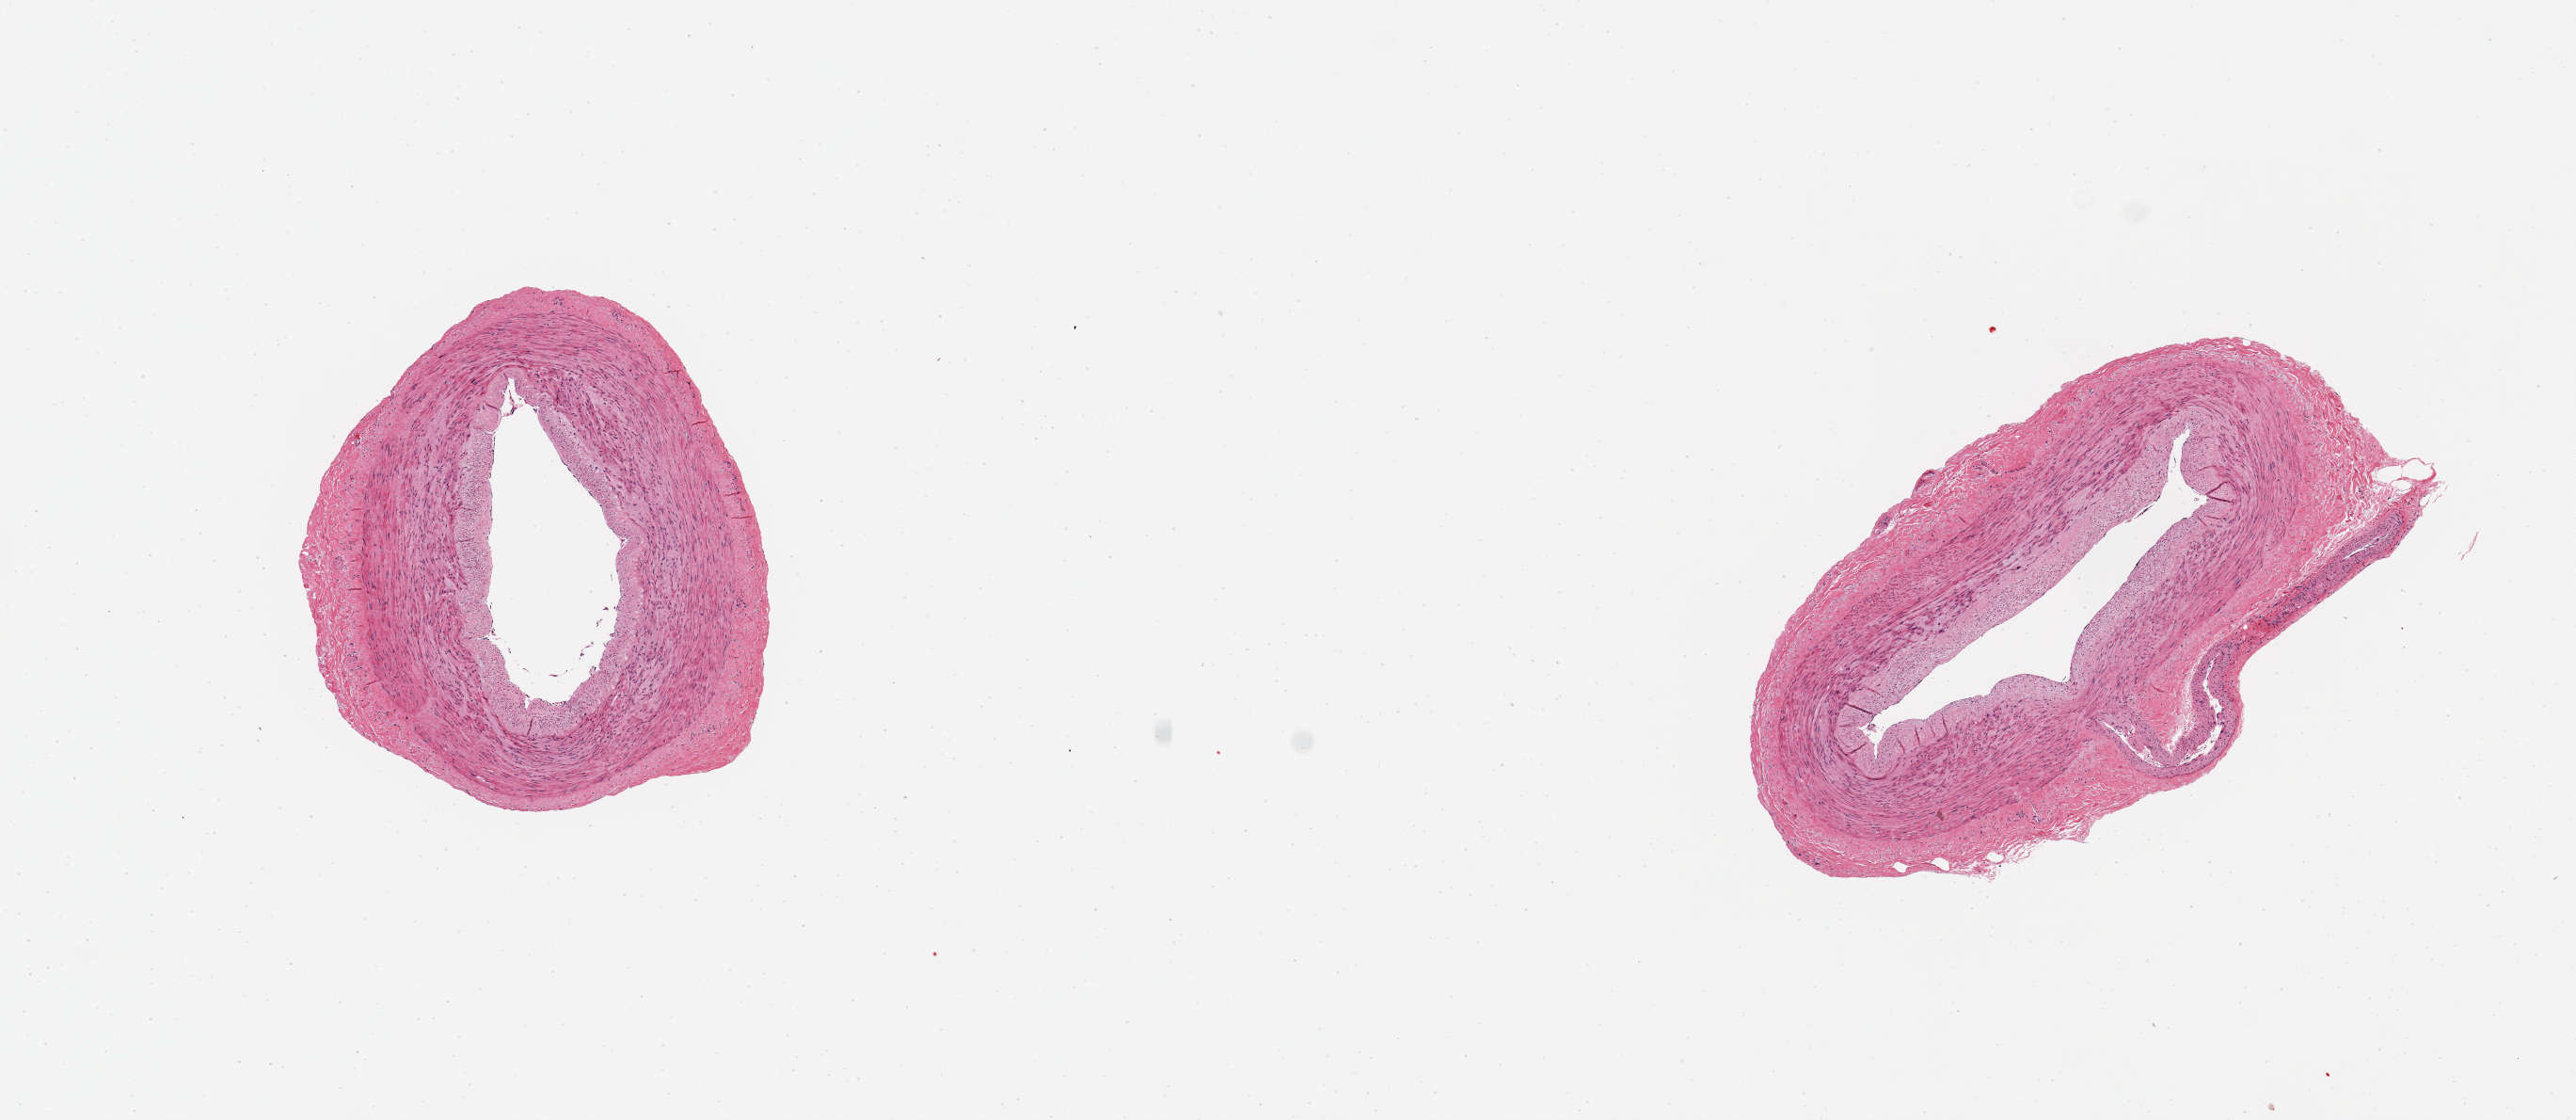
H&E whole-slide image — low-resolution overview of the scanned area, about 10.8 x 4.7 mm (acquisition: 20x scan), PAXgene-fixed, paraffin-embedded tissue, section of tibial artery (target tissue), donor tissue sample. Male donor.
- reviewer comment on this tissue sample: 2 pieces ~2mm d. Good, clean specimens